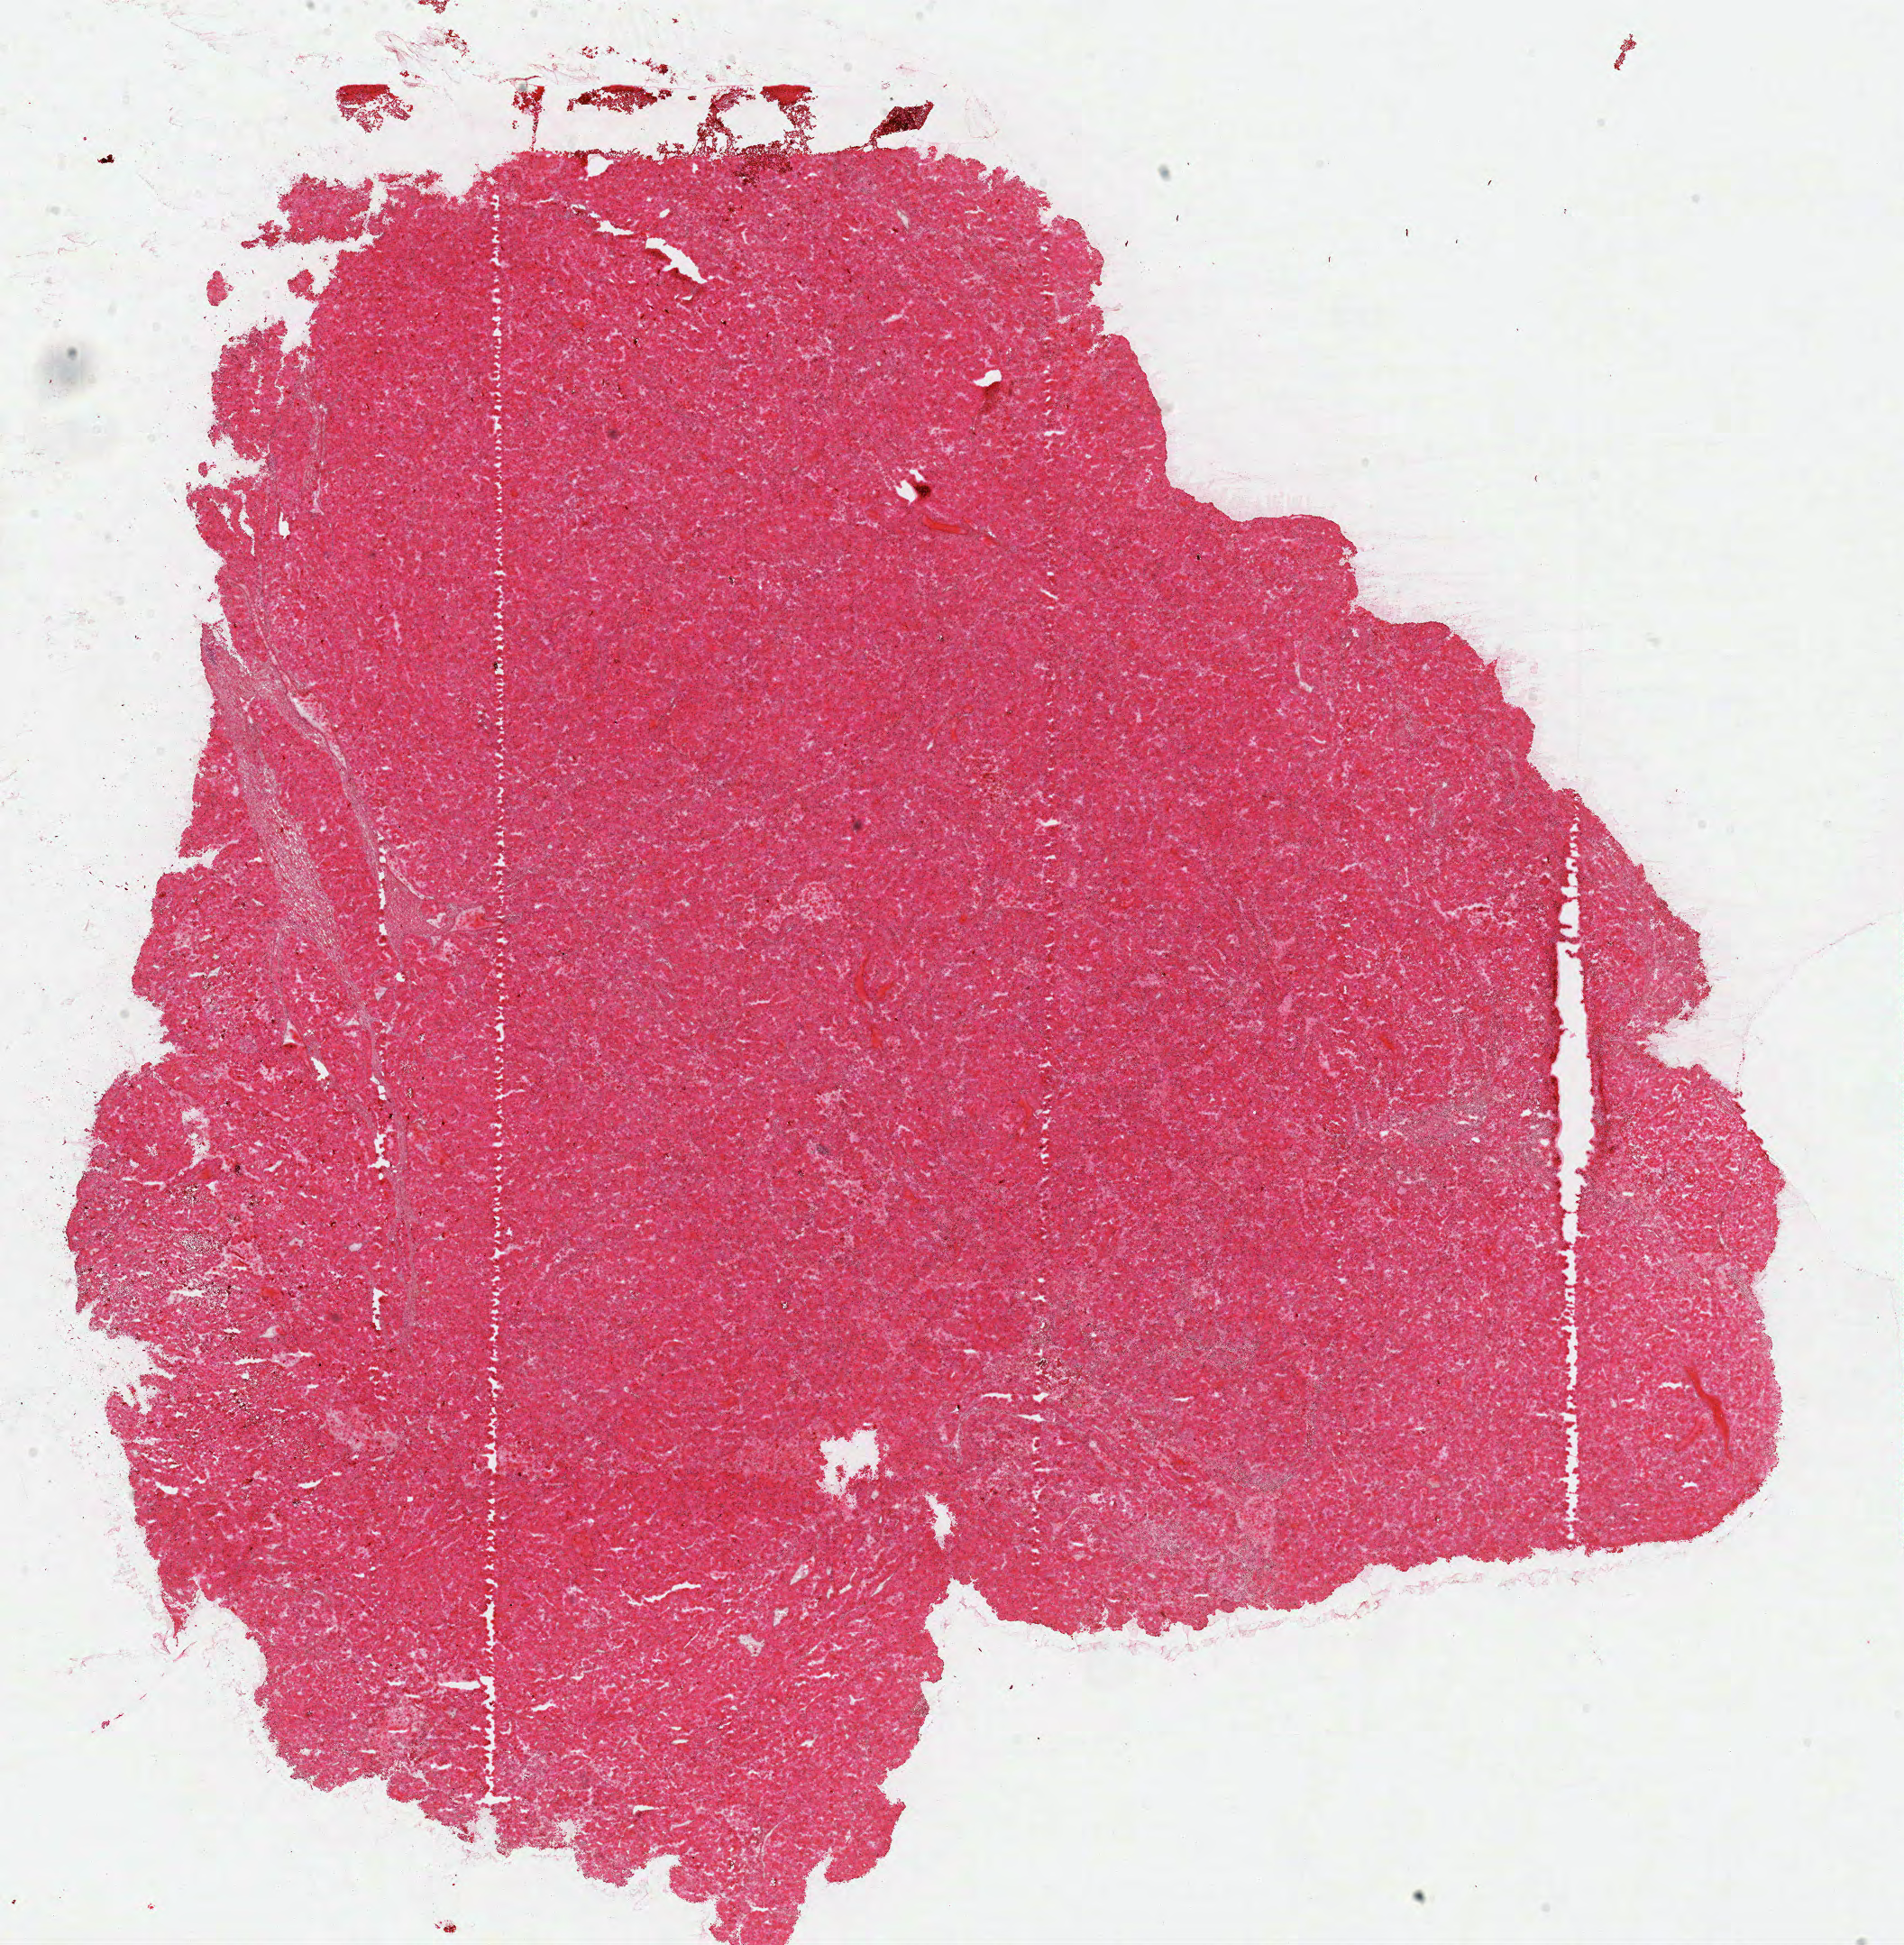
Whole-slide histology image, H&E-stained — low-resolution overview of the scanned area, about 16.6 x 17.0 mm (acquisition: 40x scan), frozen section from the top of the tissue portion, primary tumour sample from the kidney. Female patient; age at initial diagnosis 66 years. Pathologist review of this section (percent, as recorded): tumour cells 92%, tumour nuclei 85%, normal cells 0%, stromal cells 5%, necrosis 3%.
* AJCC pathologic stage: III
* TNM: T3a NX M0
* histologic diagnosis: Papillary adenocarcinoma, NOS